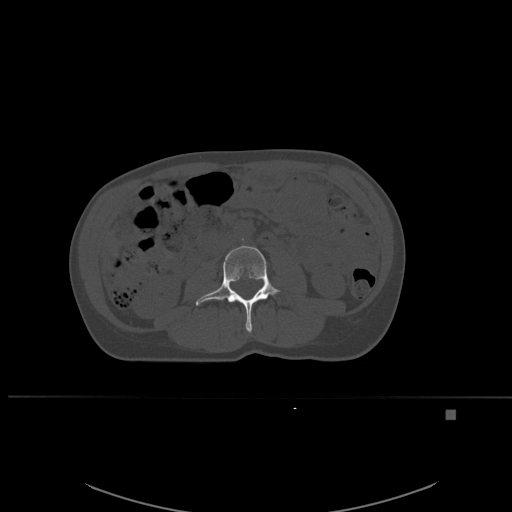
CT including the spine, one axial slice; position 214 of 537 along the scan axis; bone window (W 1800 / L 400 HU); 1.5 mm slice thickness; 512 × 512 image matrix. Patient: female, 45 years. From the clinical record (not read from this slice): primary cancer: lung.
Structures marked on this image (semi-automatically segmented with operator editing):
- L3 vertebra: bounding box (x1, y1, x2, y2) in pixels: (196, 245, 281, 333)